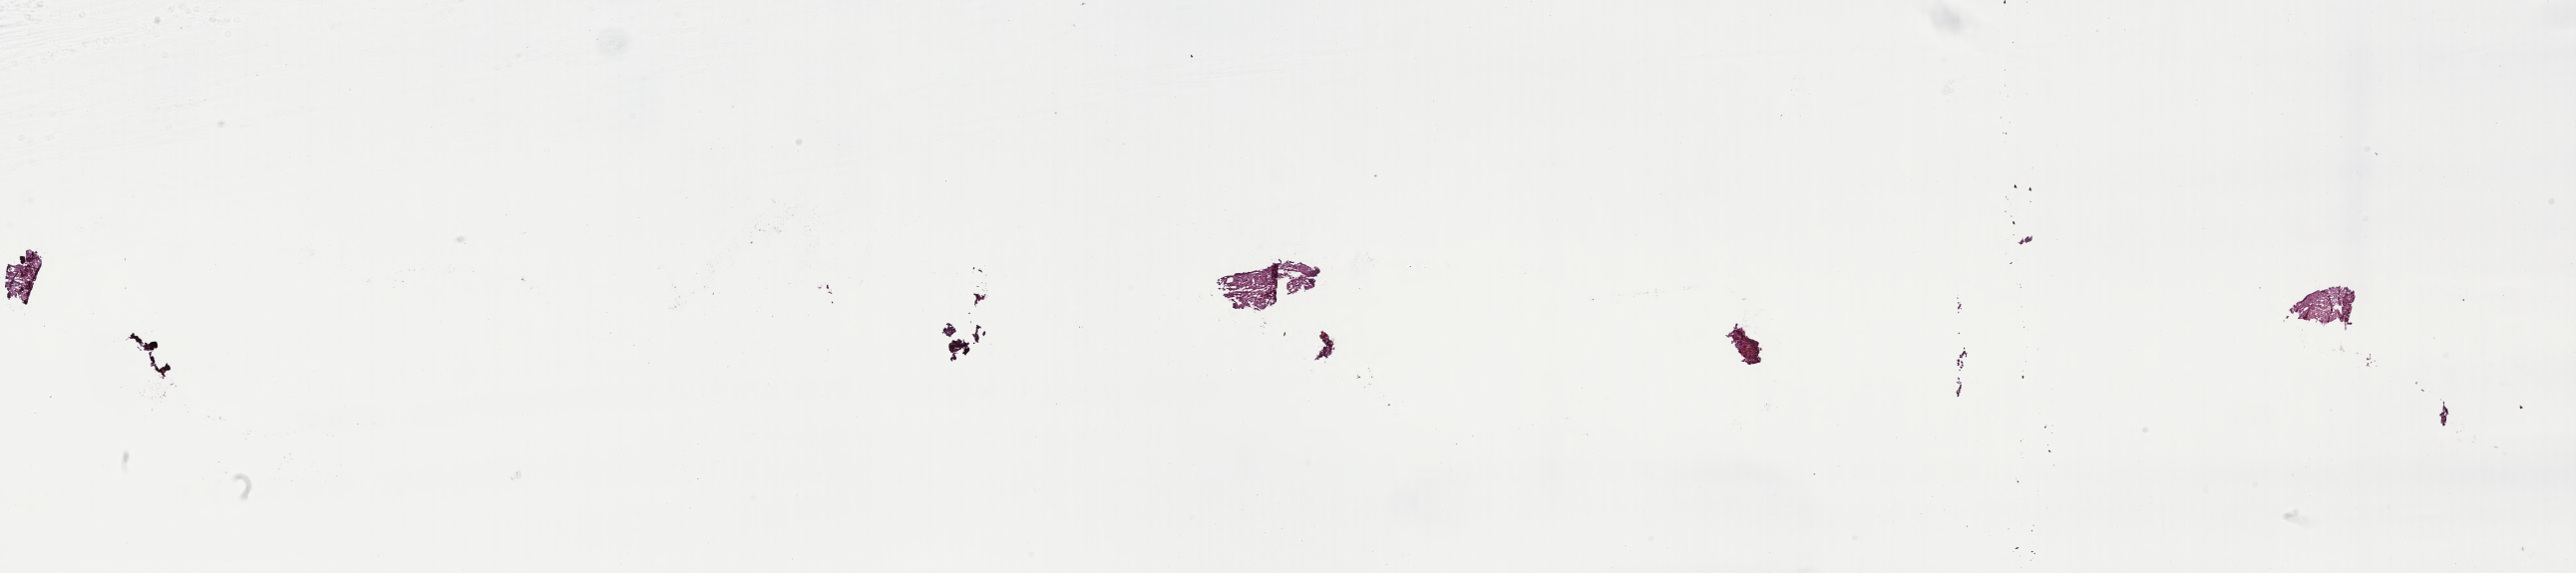
H&E whole-slide image of tumor tissue from the soft tissue of trunk — shown as a low-resolution overview of the whole scanned area (about 41.8 x 9.3 mm), frozen section (OCT-embedded). Patient female; age 51 months.
Diagnosis (ICD-O-3 morphology term): Giant cell tumor of soft parts, NOS. Tissue or organ of origin (case record): connective, subcutaneous and other soft tissues of trunk.